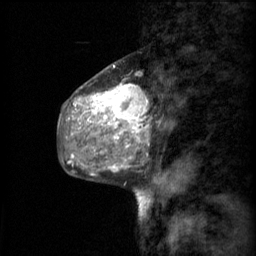
Breast MRI (dynamic contrast-enhanced), one sagittal slice. Slice 25 of 60 in the series (ordered by position). 3 images stored at this slice position (order not interpretable as contrast timing). 1.5 T. TE 4.2 ms, TR 11 ms. 2 mm slice thickness. 256 × 256 image matrix, field of view 200 × 200 mm. Female patient, age 48 years.
Outlined on this slice (semi-automatic segmentation, software-assisted and operator-edited):
- analysis volume of interest (the breast-tissue region the enhancement analysis was run in; not a lesion): bounding box <69,74,151,147> (left, top, right, bottom; pixels)
- tumour enhancement mask (voxels above the 70 % enhancement threshold inside the analysis volume of interest): <74,84,148,147>